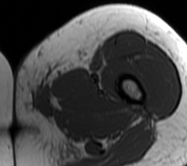
MRI of an extremity soft-tissue mass, one axial slice. Position 10 of 62 along the scan axis. MR volume resampled by the dataset authors to the PET/CT grid (not the native acquisition matrix). 3.27 mm slice thickness. 187 × 166 image matrix. Female patient. Case-level facts recorded for this patient, not image findings: histological type: leiomyosarcoma; grade: high; site of the primary tumour: groin.
Structures marked on this image (expert contour drawn on MRI and transferred to this co-registered scan by the dataset authors):
- gross tumour volume including surrounding oedema: bounding box [x1, y1, x2, y2] px = [11, 65, 69, 116]